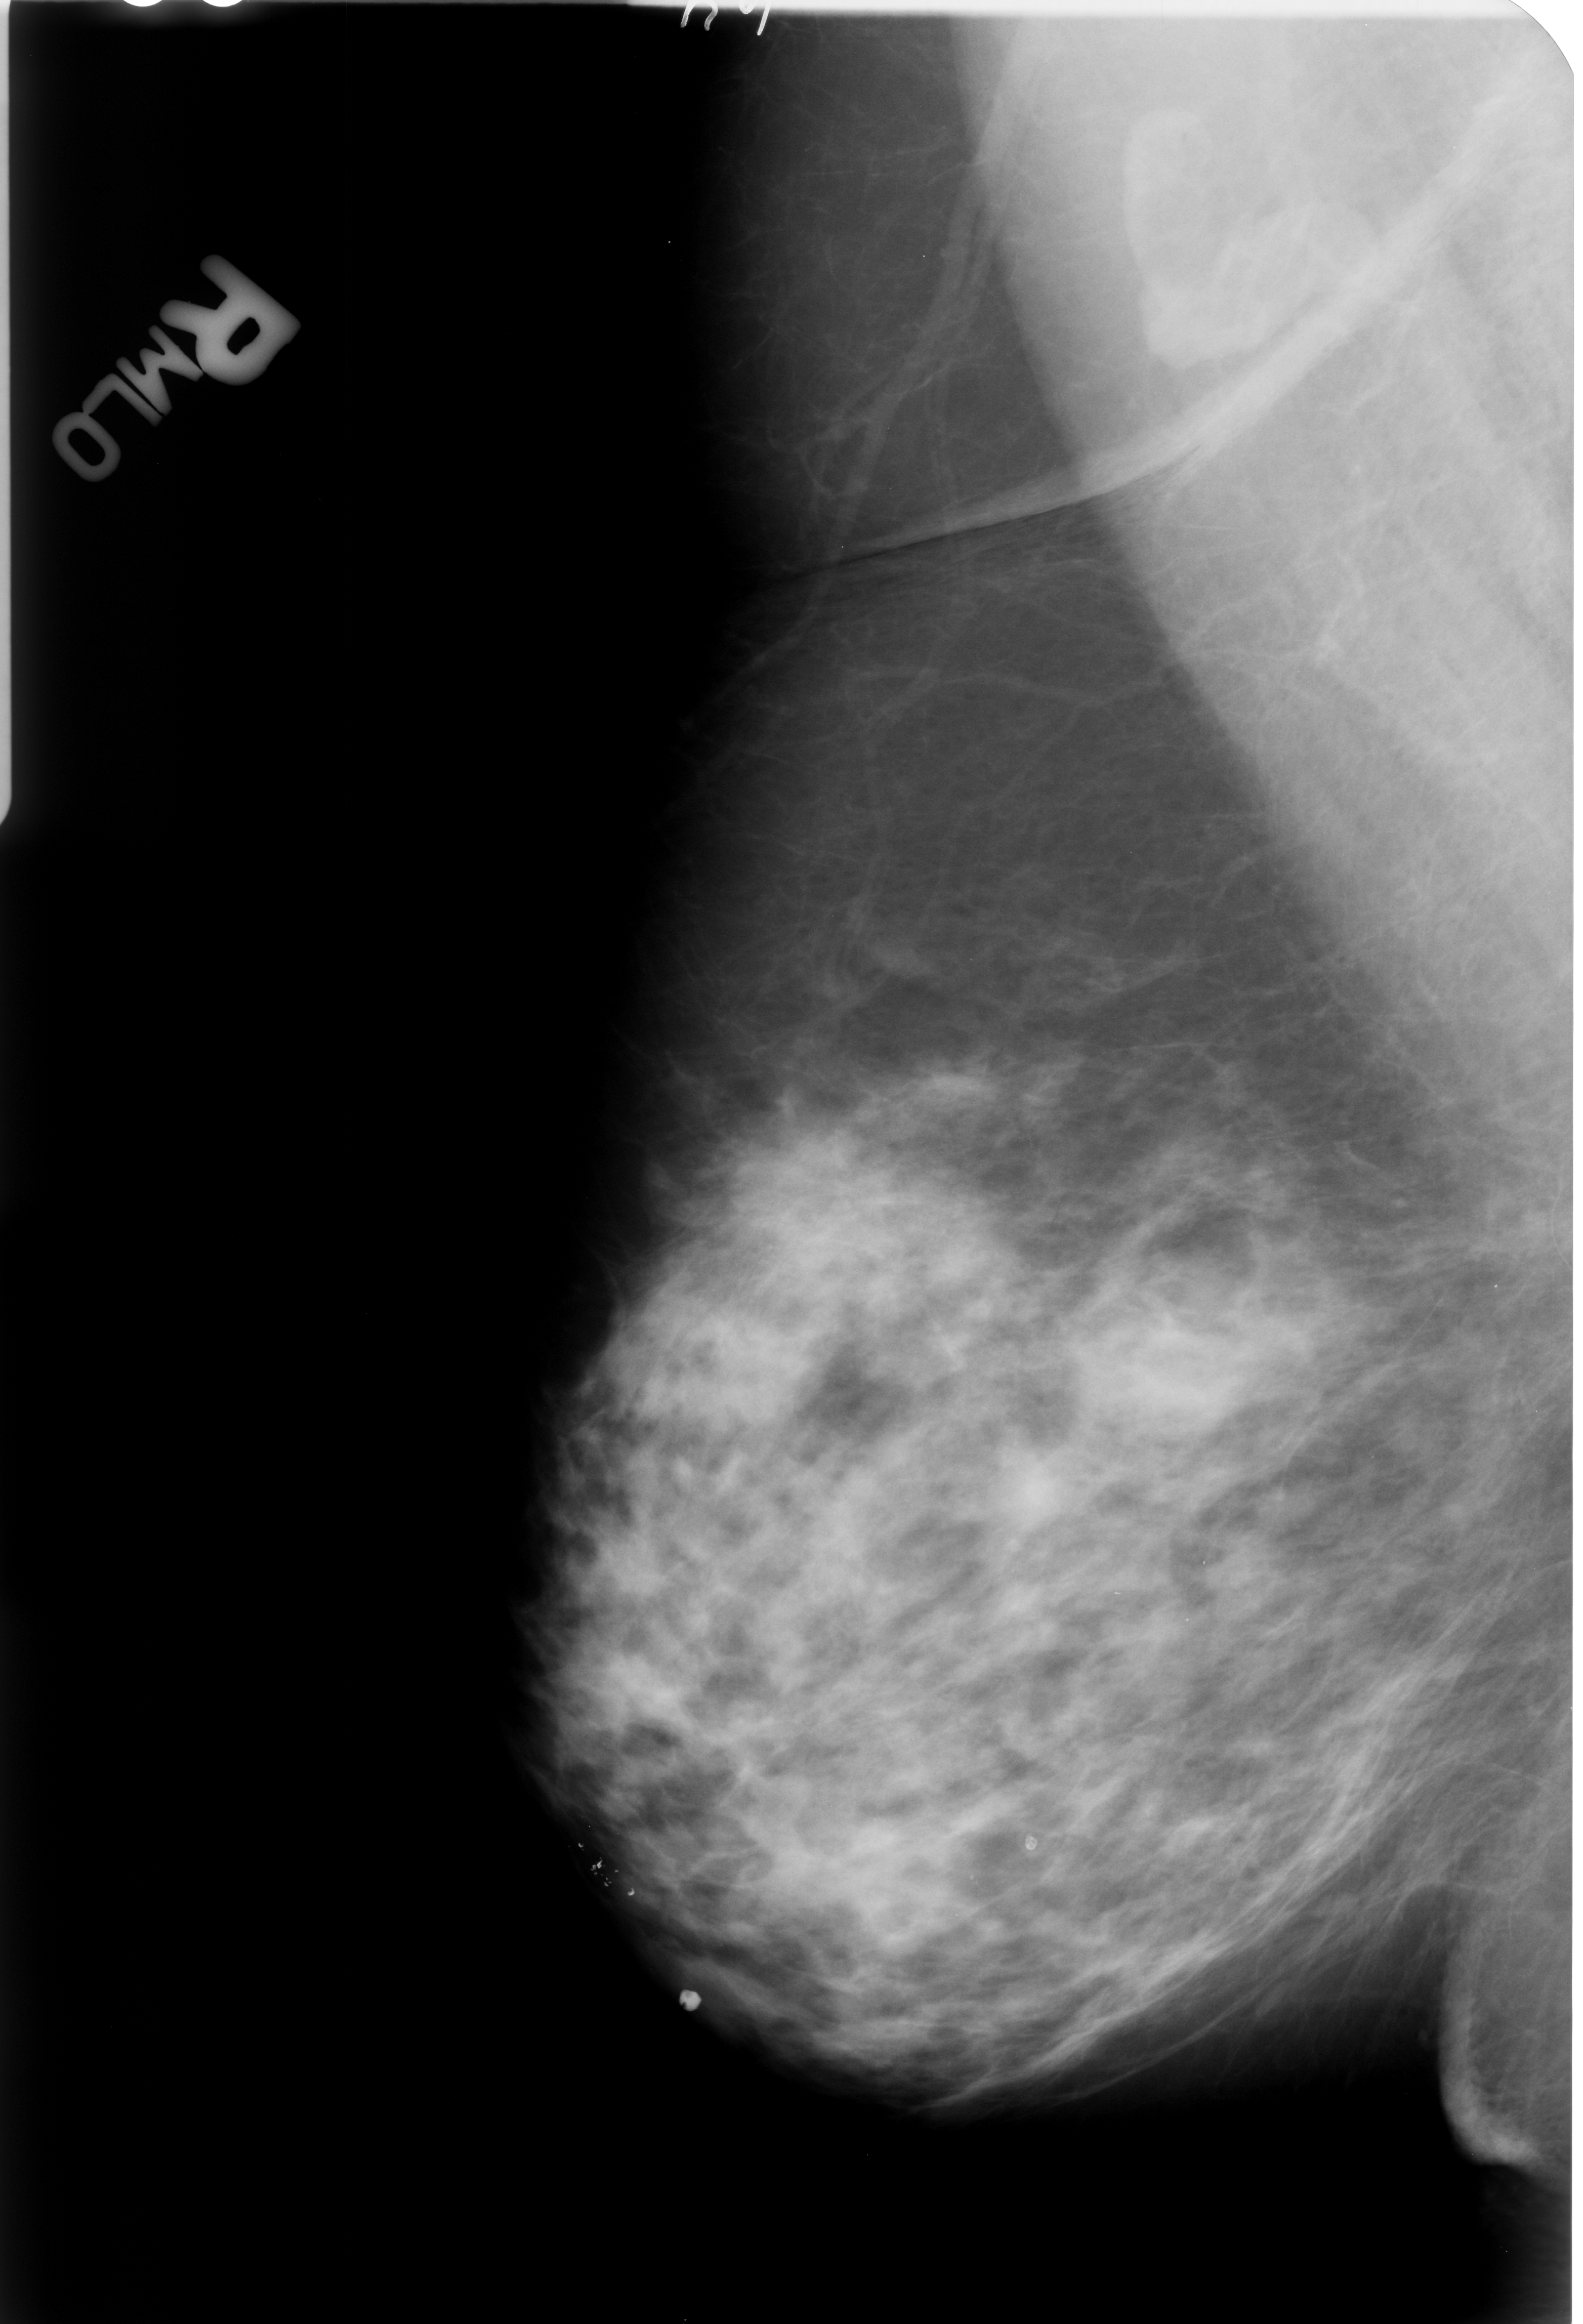
Digitized screen-film mammogram; right breast; mediolateral oblique (MLO) view; 1583 × 2324 image matrix.
Marked abnormalities (boxes around the expert regions of interest):
- Finding 1 of 2: calcifications, morphology lucent center; BI-RADS assessment category 2; outcome (as recorded, no biopsy): benign without callback (not worked up further): box from (x=821, y=2012) to (x=867, y=2065) px
- Finding 2 of 2: calcifications, morphology lucent center; BI-RADS assessment category 2; outcome (as recorded, no biopsy): benign without callback (not worked up further): (x=1012, y=1830)–(x=1041, y=1867)